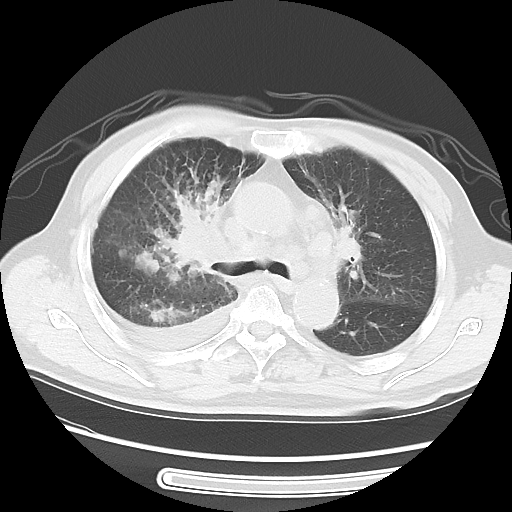
Chest CT, one axial slice; position 36 of 56 along the scan axis; lung window (W 1500 / L -600 HU); 5 mm slice thickness; 512 × 512 image matrix, field of view 360 × 360 mm. Patient: male, 77 years. From the clinical record (not read from this slice): clinical TNM (as recorded): T3 N3 M1b; histopathological grade: G3.
Structures marked on this image (rectangle marked by the reading radiologist):
- lung tumour (recorded histology: small cell carcinoma): bounding box [x1, y1, x2, y2] px = [159, 189, 230, 284]